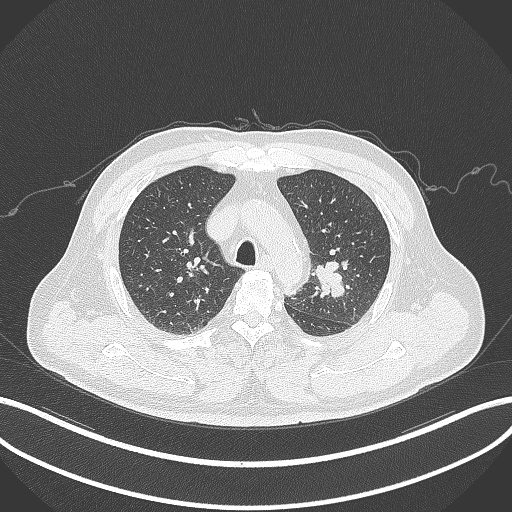
Chest CT, one axial slice; slice 228 of 286 in the series (ordered by position); reconstruction kernel B70f; lung window (W 1500 / L -600 HU); 1 mm slice thickness; 512 × 512 image matrix, field of view 400 × 400 mm. Male patient, age 67 years. From the clinical record (not read from this slice): clinical TNM (as recorded): T2a N1 M0.
Annotated regions visible in this slice (bounding box drawn by a radiologist):
- lung tumour (recorded histology: adenocarcinoma): bounding box <311,259,348,302> (left, top, right, bottom; pixels)